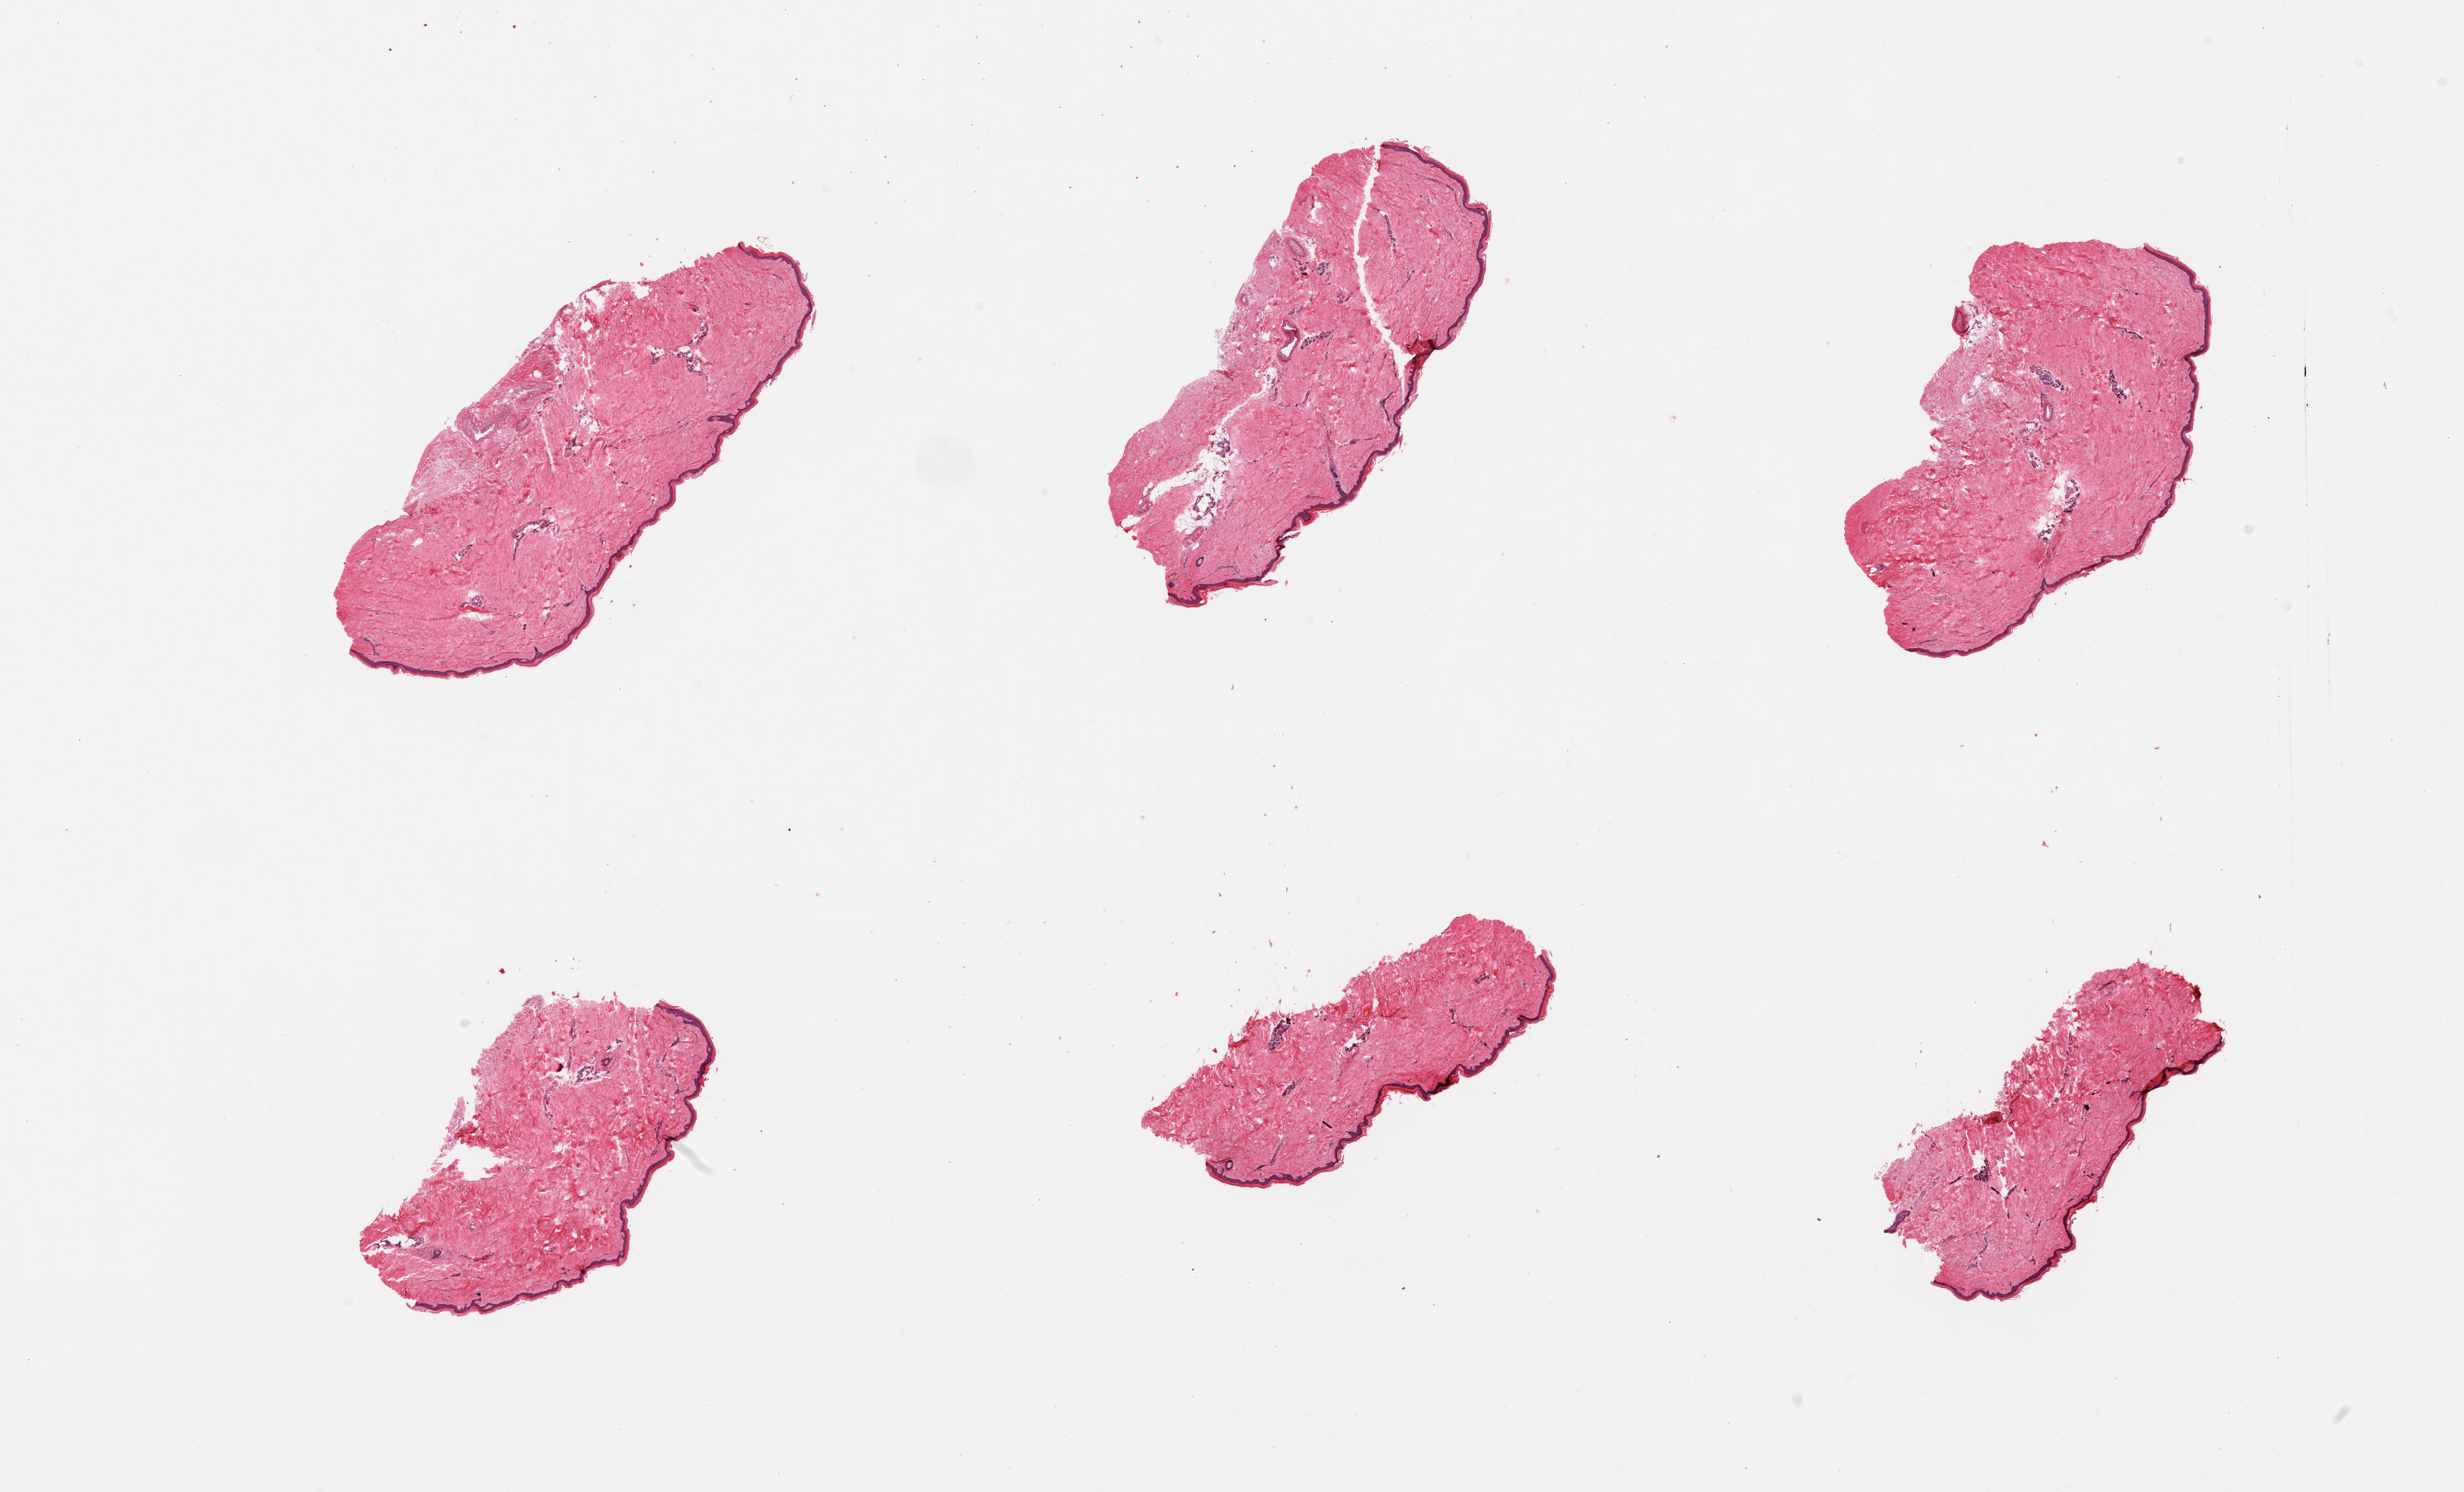
Whole-slide image, haematoxylin and eosin stain, a low-resolution overview of the entire scanned area, about 25.6 x 15.5 mm, PAXgene-fixed paraffin-embedded (PFPE) section, sampled site (target tissue): skin of lower leg, tissue donor sample. Donor sex: female.
Pathologist's review note for this sample: 6 pieces; well trimmed, epidermis measures 34 microns.